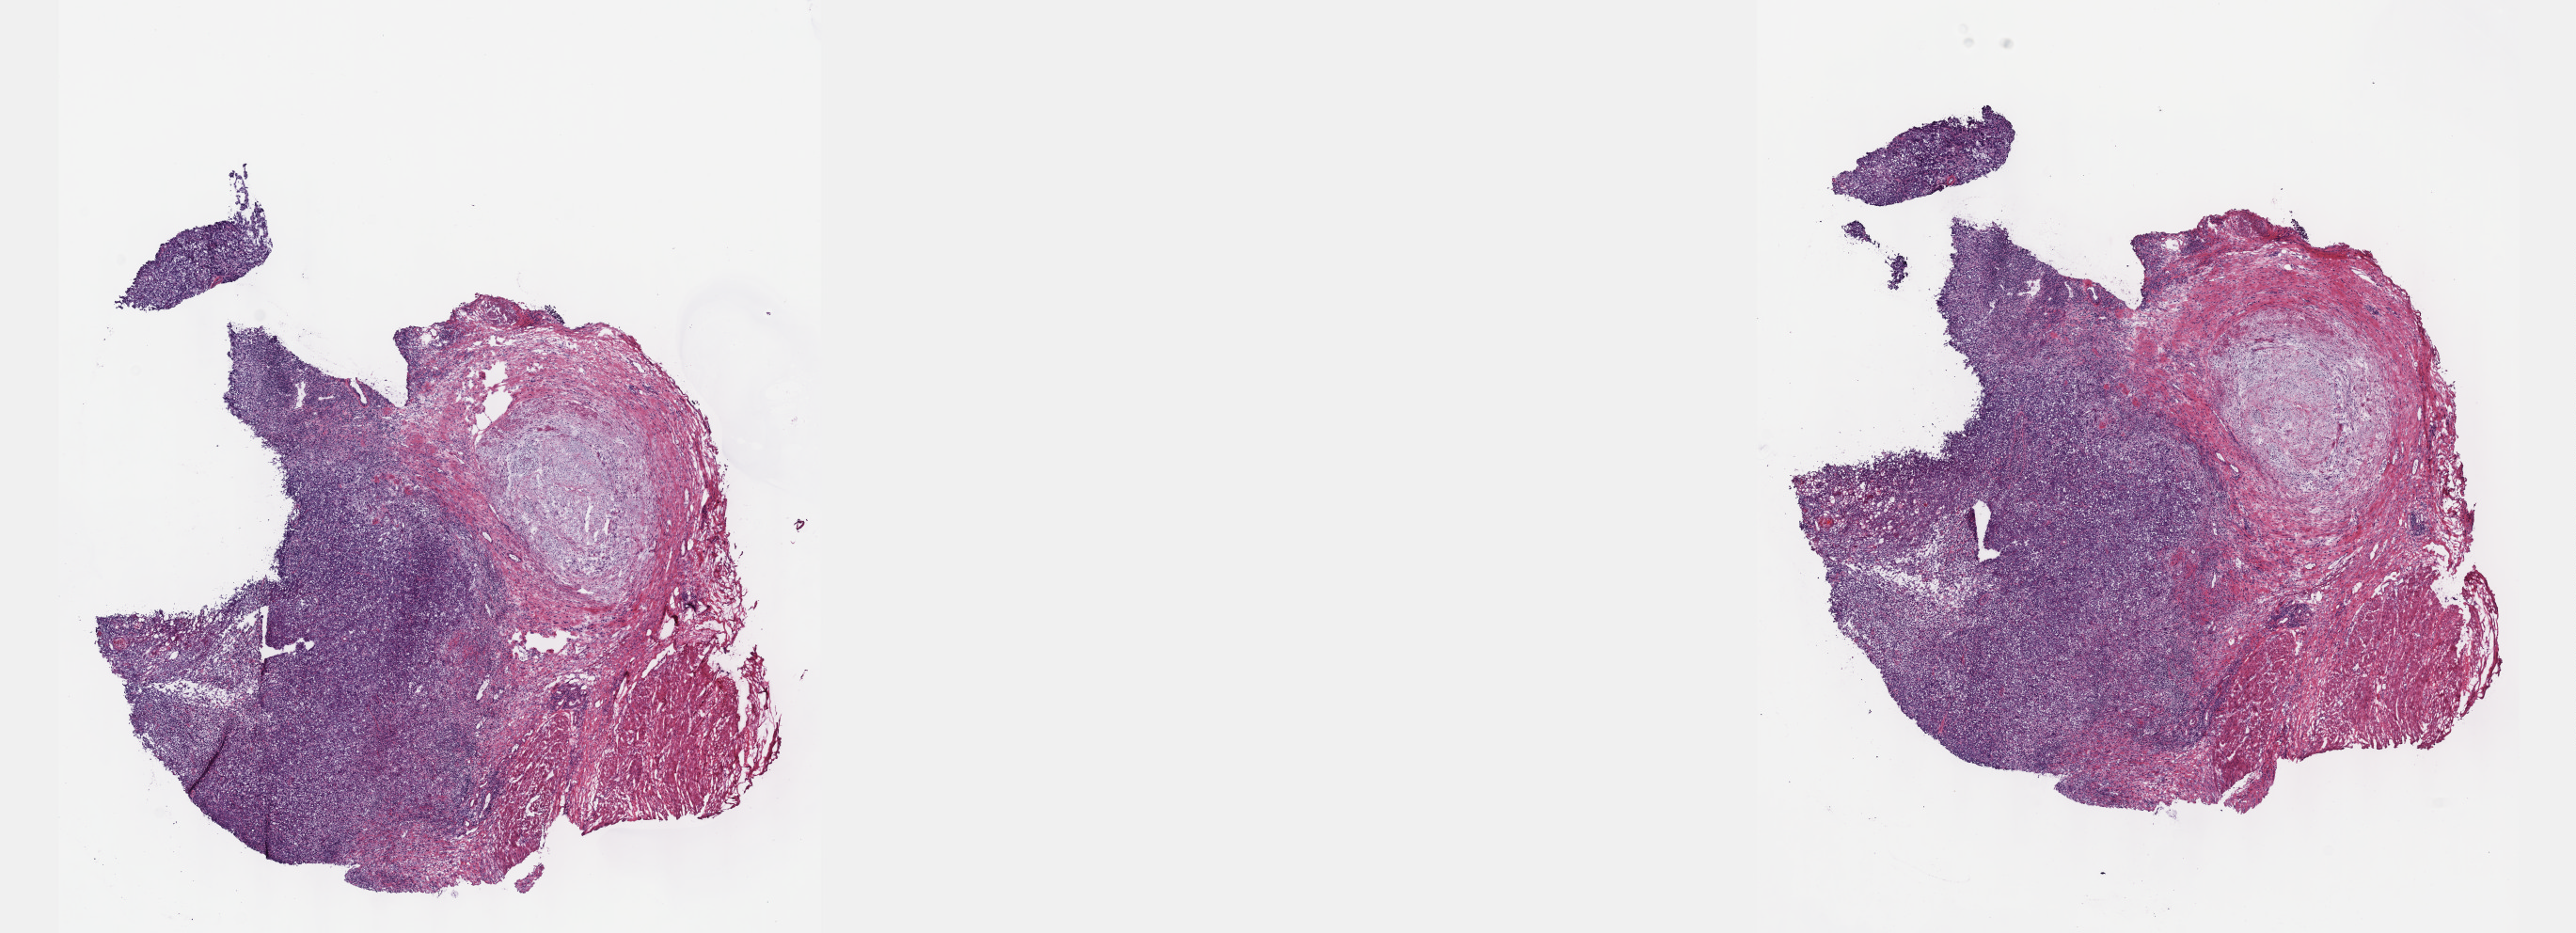
Whole-slide histology image, H&E-stained, a low-resolution overview of the entire scanned area, about 22.1 x 8.0 mm (from a 40x scan), frozen section from the top of the tissue portion, sample: primary tumour, bladder. Female, age 75 years at initial diagnosis. Histologic grade: high grade. Slide review estimates, as recorded: tumour cells 60%, tumour nuclei 60%, normal cells 40%, stromal cells 0%, necrosis 0%. Inflammatory infiltration, as recorded: lymphocyte infiltration 5%, monocyte infiltration 0%, neutrophil infiltration 0%.
* pathologic diagnosis: Transitional cell carcinoma (posterior wall of bladder)
* AJCC pathologic stage: IV (6th edition)